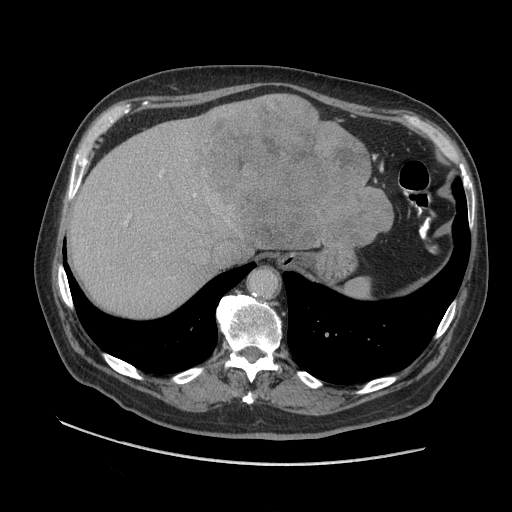
Contrast-enhanced abdominal CT (liver protocol), one axial slice; position 76 of 109 along the scan axis; 140 kVp; soft-tissue window (W 400 / L 40 HU); 2.5 mm slice thickness; 512 × 512 image matrix, field of view 420 × 420 mm. Case-level facts recorded for this patient, not image findings: diagnosis: hepatocellular carcinoma (patient treated with transarterial chemoembolisation; whether this scan precedes or follows treatment is not stated here); TNM stage (as recorded): Stage-I; Child-Pugh class: A; tumour nodularity: uninodular.
Annotated regions visible in this slice (semi-automatically segmented with operator editing):
- abdominal aorta: box from (x=250, y=268) to (x=276, y=297) px
- liver parenchyma outside the tumour (the mass and vessels are separate outlines, so this box may not span the whole liver): (x=68, y=102)–(x=352, y=317)
- mass: (x=192, y=93)–(x=393, y=256)
- liver vessels: (x=125, y=169)–(x=196, y=224)